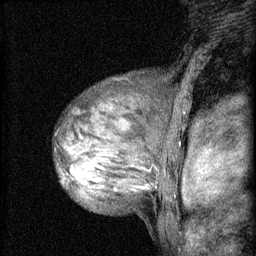
Breast MRI (dynamic contrast-enhanced), one sagittal slice. 3 images stored at this slice position (order not interpretable as contrast timing). 1.5 T. TE 4.2 ms, TR 8.2 ms. 2 mm slice thickness. 256 × 256 image matrix, field of view 180 × 180 mm. Patient: female, 48 years.
Outlined on this slice (semi-automatic segmentation, software-assisted and operator-edited):
- analysis volume of interest (the breast-tissue region the enhancement analysis was run in; not a lesion): bounding box (x1, y1, x2, y2) in pixels: (58, 138, 133, 191)
- tumour enhancement mask (voxels above the 70 % enhancement threshold inside the analysis volume of interest): (70, 152, 103, 183)